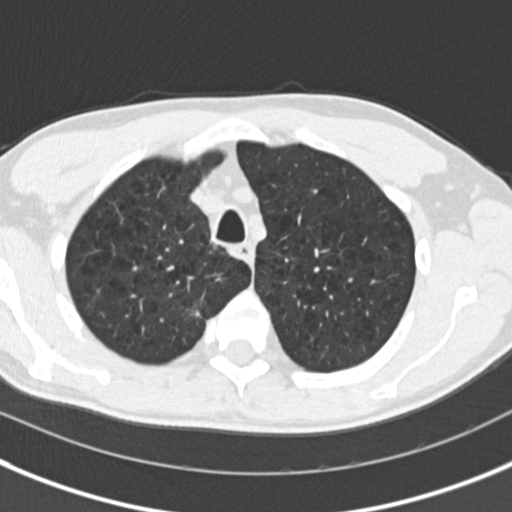
Low-dose screening chest CT, one axial slice. Slice 140 of 175 in the series (ordered by position). Reconstruction kernel B30f. 120 kVp. Lung window (W 1500 / L -600 HU). 2 mm slice thickness. 512 × 512 image matrix, field of view 306 × 306 mm.
Structures marked on this image (outlined manually by an expert reader):
- lesion 2 (tumor, upper lobe of right lung): box from (x=195, y=311) to (x=200, y=316) px